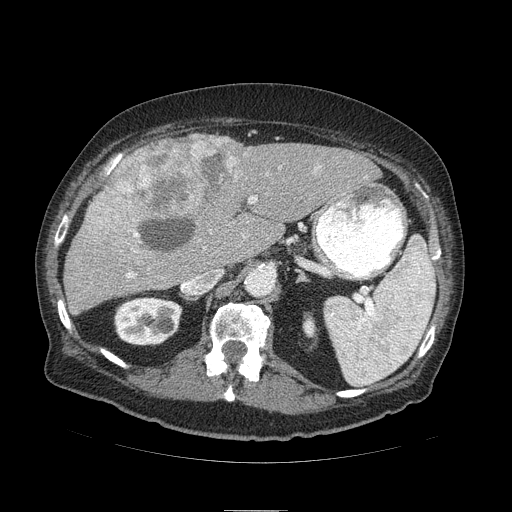
Contrast-enhanced abdominal CT (liver protocol), one axial slice; slice 57 of 103 in the series (ordered by position); reconstruction kernel STANDARD; 120 kVp; soft-tissue window (W 400 / L 40 HU); 512 × 512 image matrix, field of view 440 × 440 mm. Case-level facts recorded for this patient, not image findings: diagnosis: hepatocellular carcinoma (patient treated with transarterial chemoembolisation; whether this scan precedes or follows treatment is not stated here); TNM stage (as recorded): Stage-IIIA; Child-Pugh class: B.
Annotated regions visible in this slice (semi-automatic segmentation, software-assisted and operator-edited):
- liver parenchyma outside the tumour (the mass and vessels are separate outlines, so this box may not span the whole liver): box from (x=64, y=136) to (x=380, y=314) px
- mass: (x=78, y=133)–(x=246, y=251)
- liver vessels: (x=127, y=166)–(x=320, y=278)